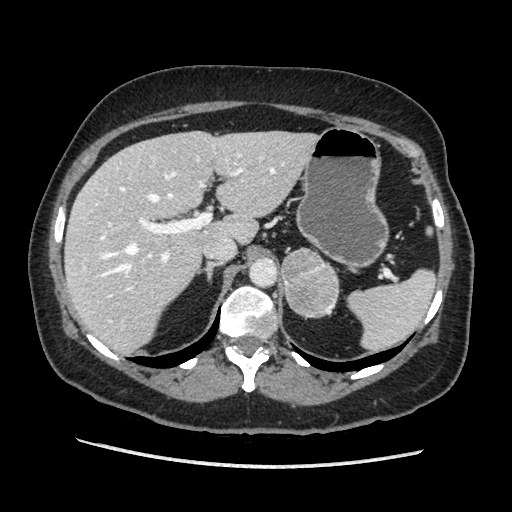
Contrast-enhanced abdominal CT, one axial slice. Position 133 of 203 along the scan axis. Soft-tissue window (W 400 / L 40 HU). 1.25 mm slice thickness. 512 × 512 image matrix, field of view 360 × 360 mm. Female patient. Case-level facts recorded for this patient, not image findings: diagnosis: adrenocortical carcinoma; tumour side: left adrenal; tumour size at pathology: 6.5 cm; Ki-67 index: 22 %; stage (as recorded): 2.
Structures marked on this image (semi-automatically segmented with operator editing):
- mass: bounding box [x1, y1, x2, y2] px = [282, 248, 339, 317]